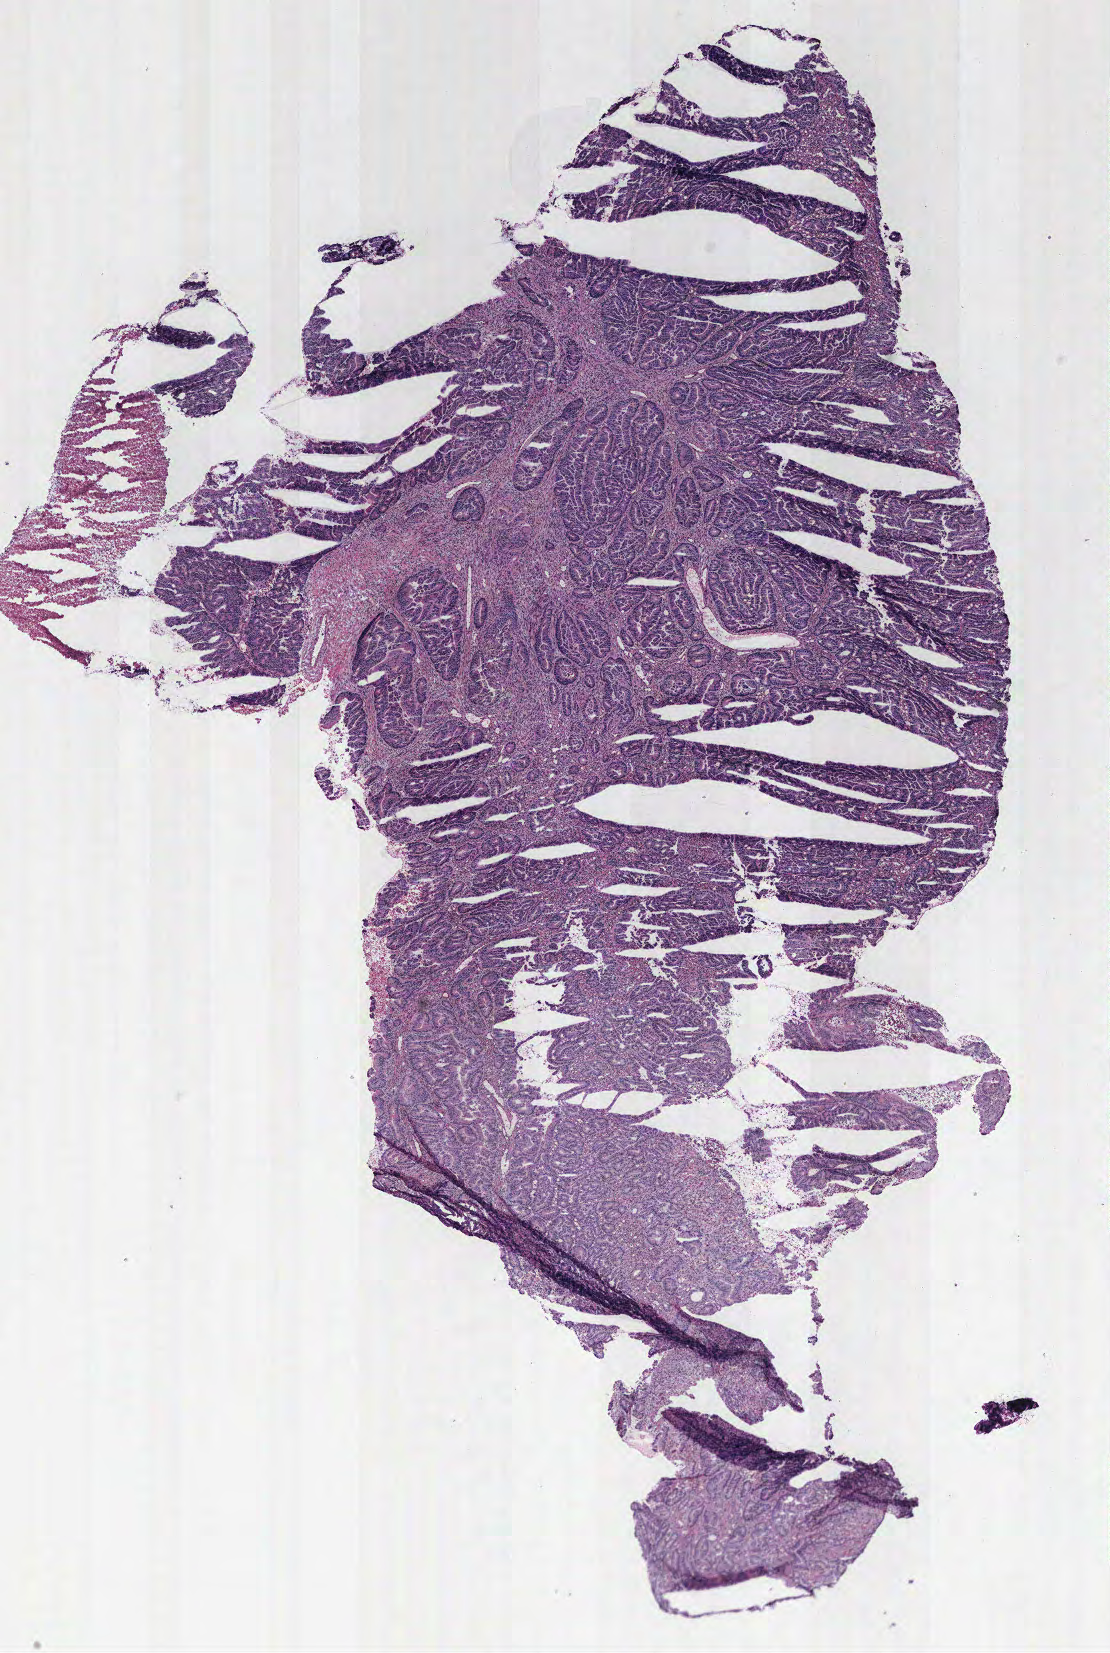
Digitized Hematoxylin and eosin (H&E) stained tissue section (whole slide), a low-resolution overview of the entire scanned area, about 8.9 x 13.2 mm (slide scanned at 40x). Colon, tumour tissue. 56-year-old male patient.
Diagnosis: Adenocarcinoma, NOS. AJCC pathologic stage: I. Primary tumour site (as recorded): colon.